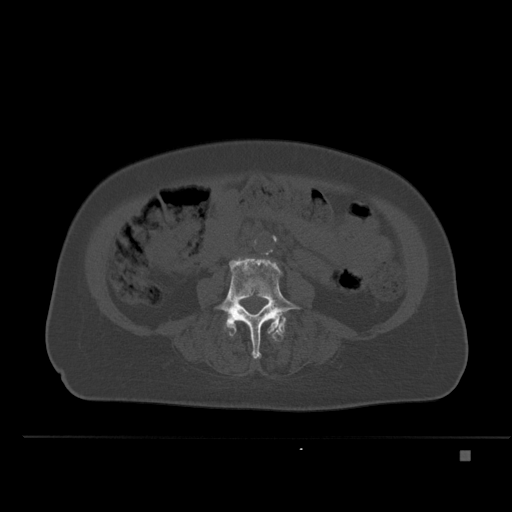
CT including the spine, one axial slice. Slice 179 of 477 in the series (ordered by position). Bone window (W 1800 / L 400 HU). 1.5 mm slice thickness. 512 × 512 image matrix. Patient: female, 74 years. From the clinical record (not read from this slice): primary cancer: colon.
Structures marked on this image (semi-automatic segmentation, software-assisted and operator-edited):
- L4 vertebra: bounding box [x1, y1, x2, y2] px = [216, 258, 301, 359]
- L5 vertebra: [226, 321, 286, 341]